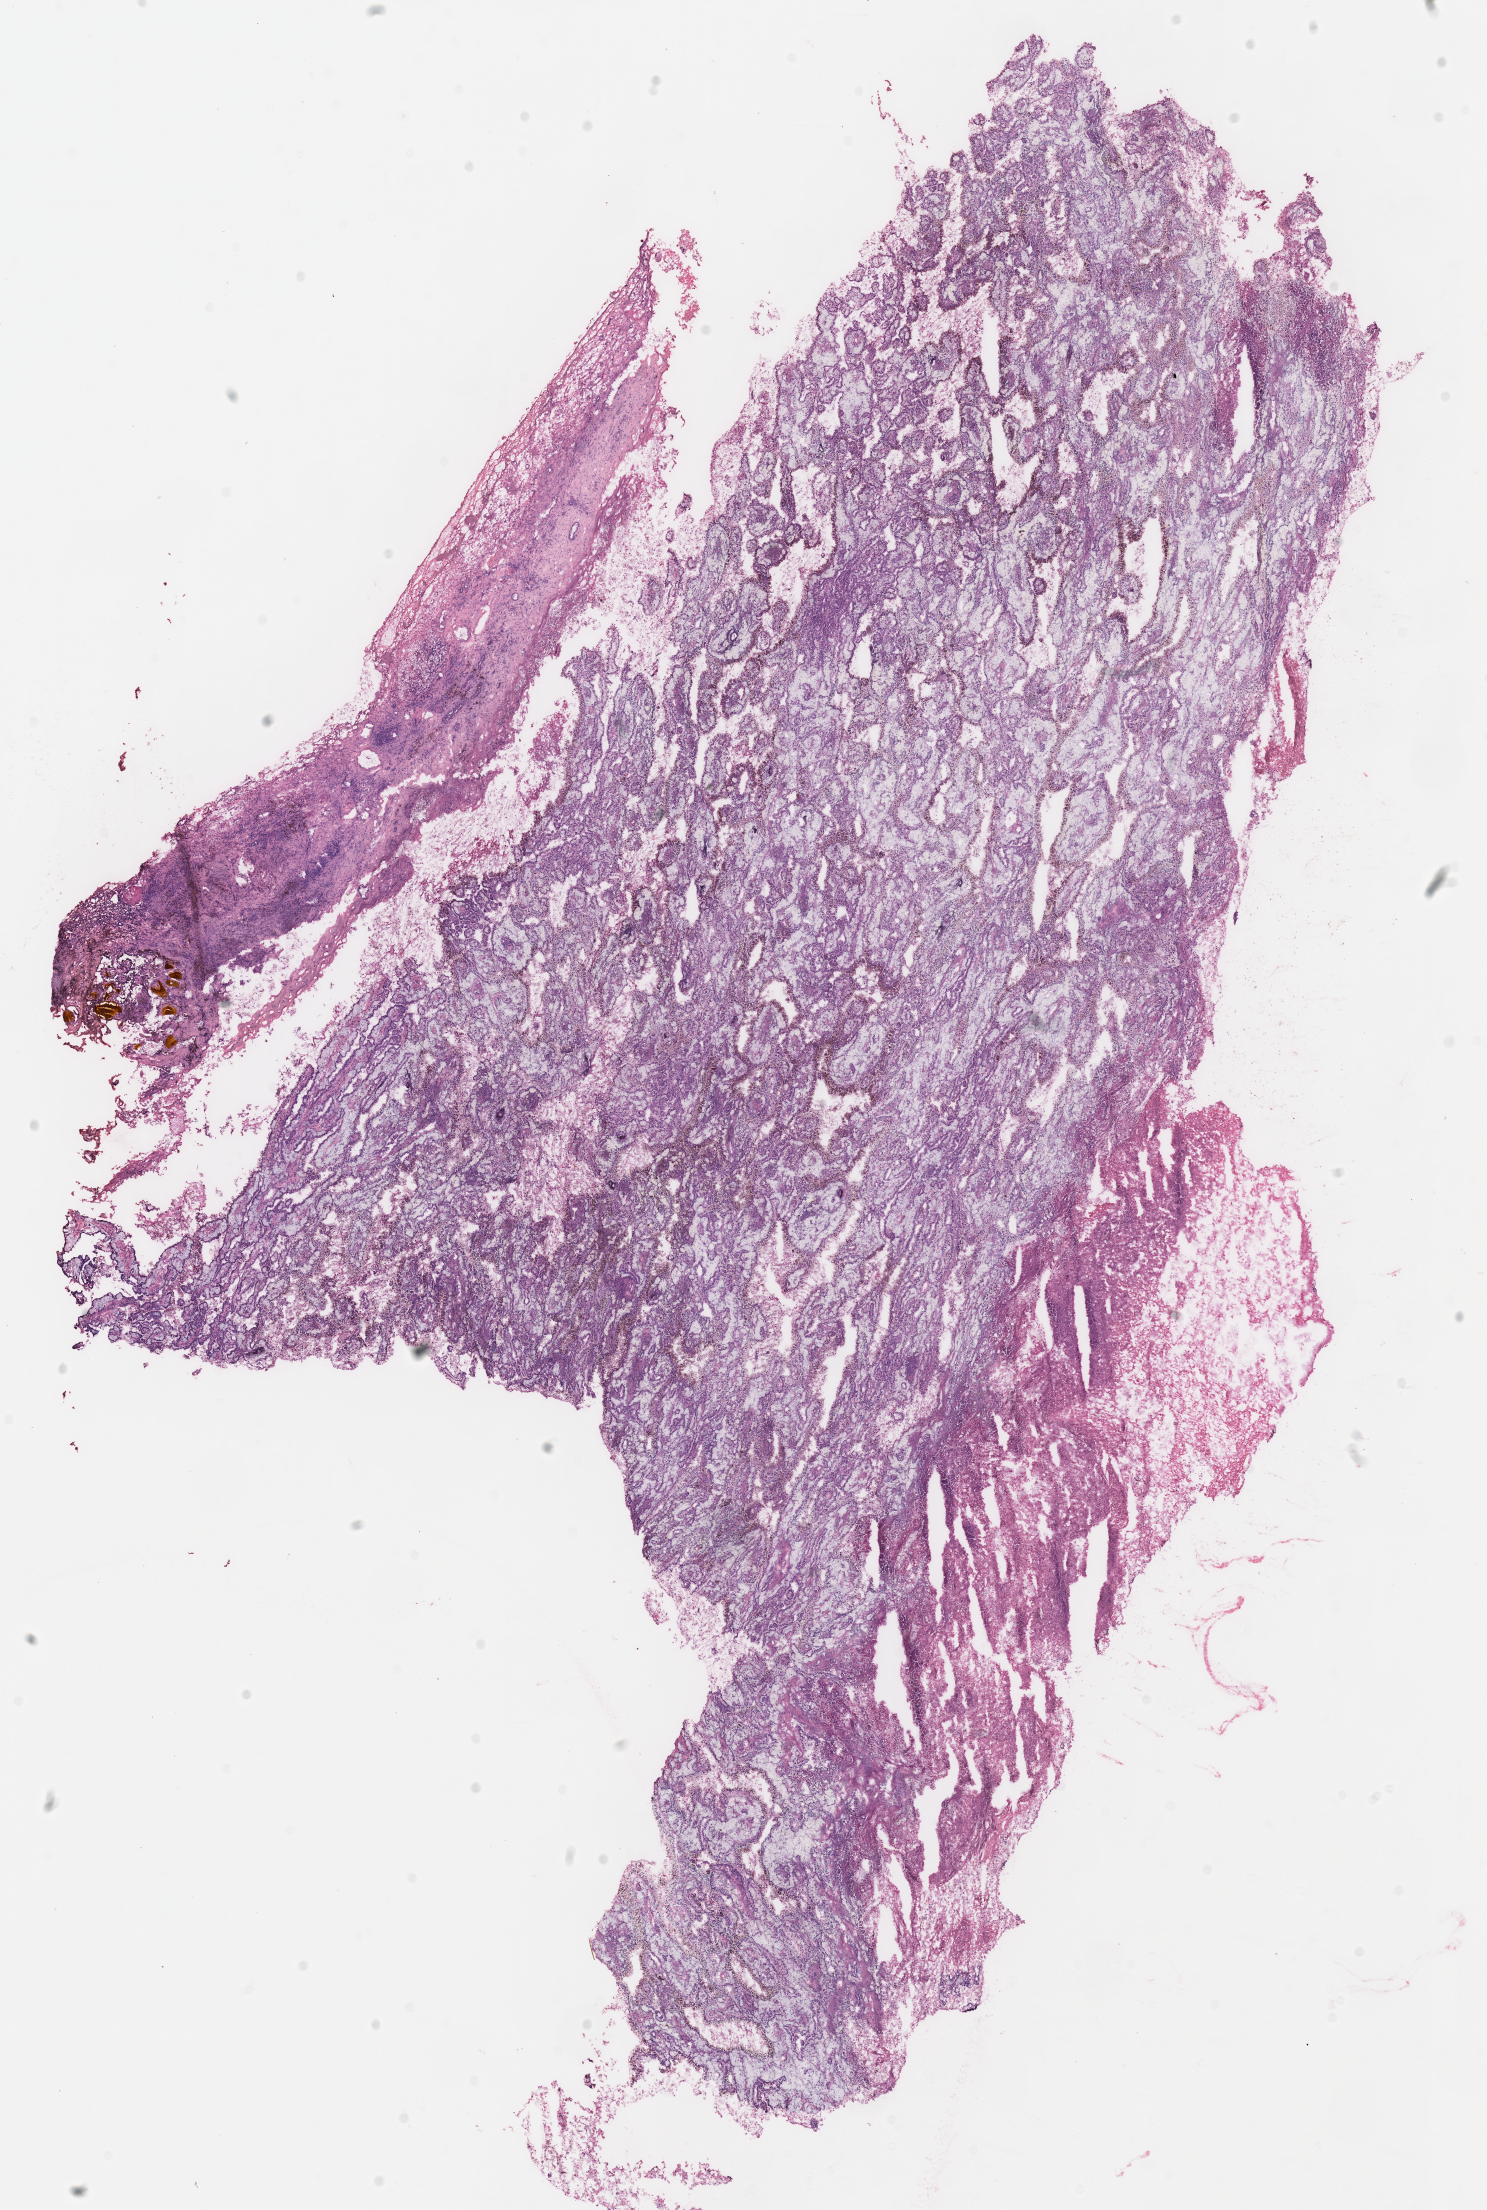
Whole-slide histology image, Hematoxylin and eosin (H&E) stained, a low-resolution overview of the entire scanned area, about 11.7 x 17.4 mm, frozen section, primary tumour sample from the kidney. Patient: male, age at initial diagnosis 66 years. Composition of this section per pathologist review: tumour cells 70%, tumour nuclei 70%, normal cells 0%, stromal cells 10%, necrosis 20%. Inflammatory infiltration, as recorded: lymphocyte infiltration 0%, monocyte infiltration 19%, neutrophil infiltration 0%.
Diagnosis: Papillary adenocarcinoma, NOS. AJCC pathologic stage: I. Laterality: left.